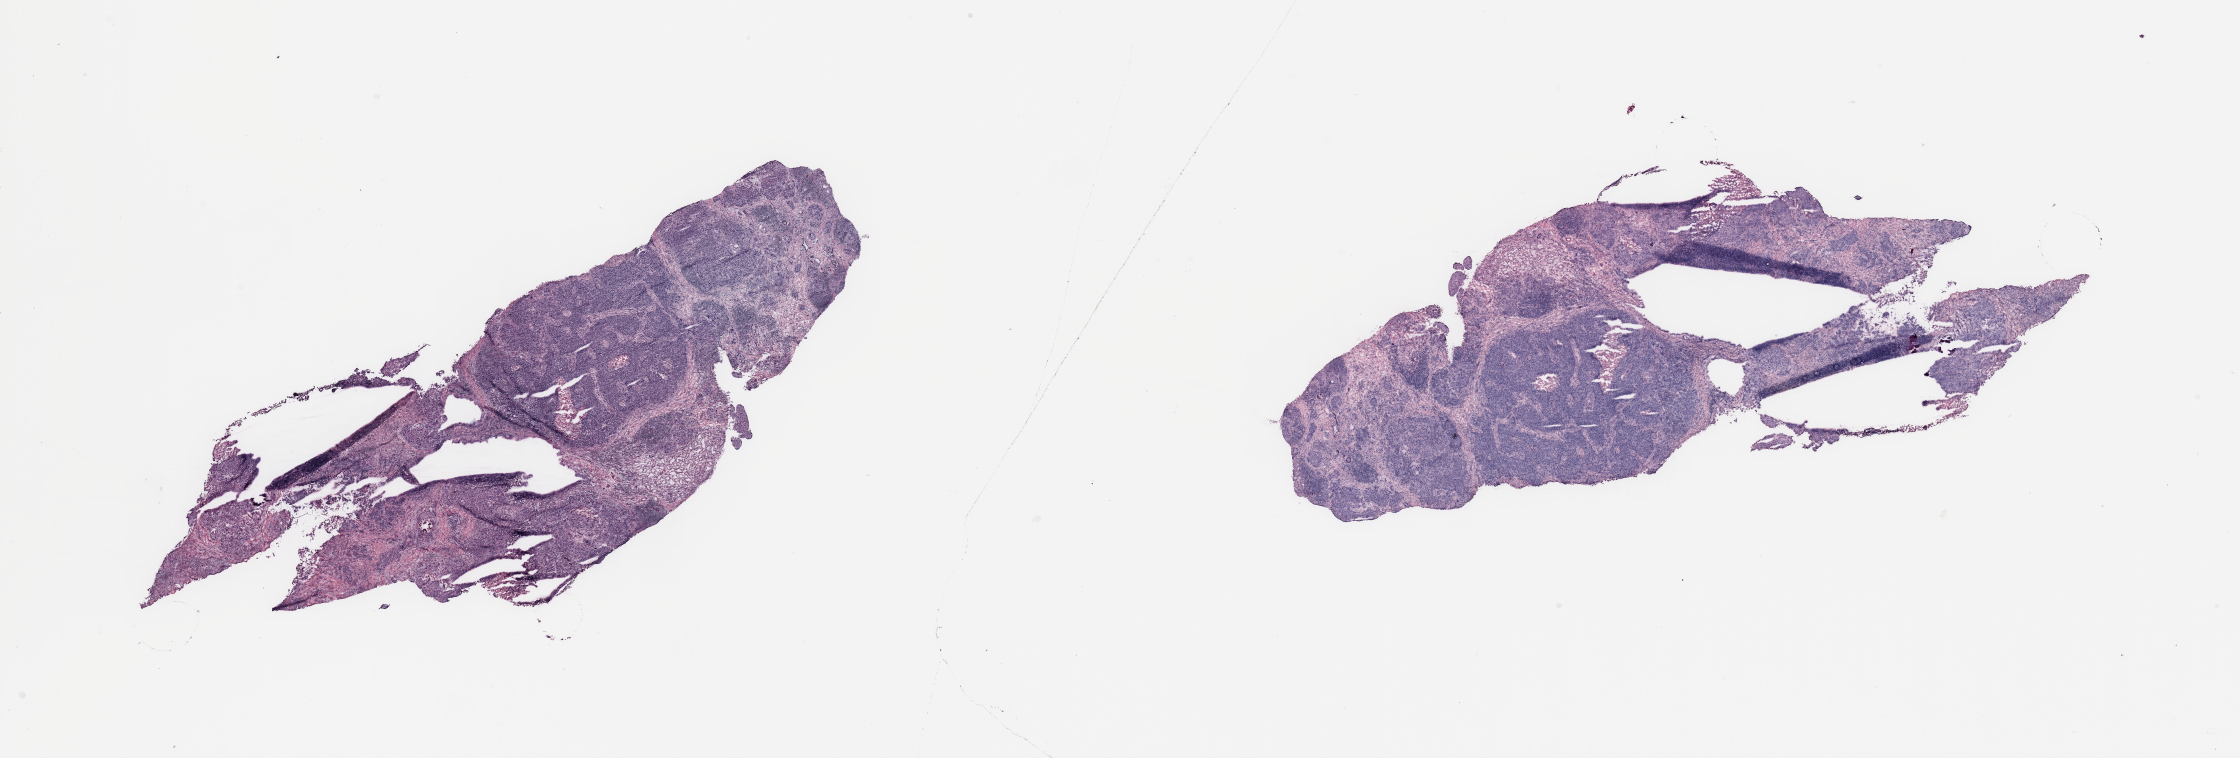
Whole-slide histology image, H&E-stained — shown as a low-resolution overview of the whole scanned area (about 35.4 x 12.0 mm, slide scanned at 20x); breast, tumour tissue. Patient: female, age 40 years.
Histologic diagnosis: Infiltrating duct carcinoma, NOS.